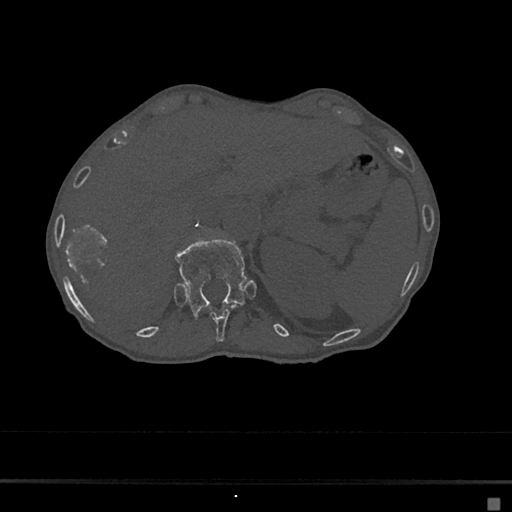
CT including the spine, one axial slice. Position 136 of 797 along the scan axis. Reconstruction kernel Br40s/3. 120 kVp. Bone window (W 1800 / L 400 HU). 512 × 512 image matrix, field of view 360 × 360 mm. Patient: female, 68 years. From the clinical record (not read from this slice): primary cancer: renal.
Structures marked on this image (semi-automatically segmented with operator editing):
- T11 vertebra: box from (x=210, y=309) to (x=232, y=342) px
- T12 vertebra: (x=175, y=237)–(x=248, y=312)